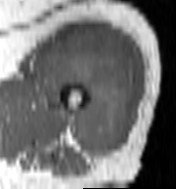
MRI of an extremity soft-tissue mass, one axial slice. Slice 73 of 100 in the series (ordered by position). MR volume resampled by the dataset authors to the PET/CT grid (not the native acquisition matrix). 3.27 mm slice thickness. 176 × 189 image matrix, field of view 172 × 185 mm. Female patient. Case-level facts recorded for this patient, not image findings: histological type: undifferentiated – high grade; grade: high; site of the primary tumour: left thigh.
Structures marked on this image (expert contour drawn on MRI and transferred to this co-registered scan by the dataset authors):
- gross tumour volume including surrounding oedema: bounding box [x1, y1, x2, y2] px = [44, 34, 134, 158]
- gross tumour volume (mass): [44, 34, 134, 158]